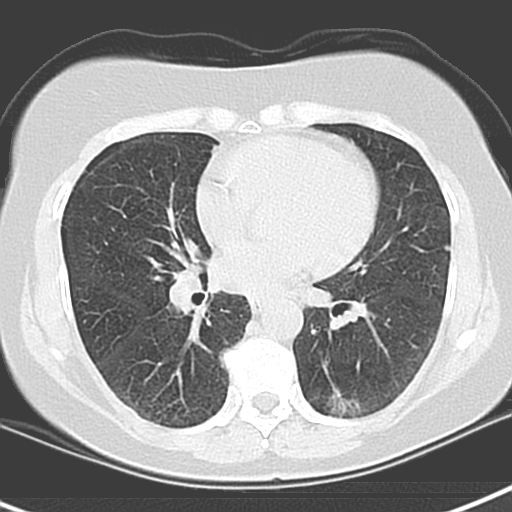
Axial slice from a low-dose chest CT screening exam, first (baseline) screen, lung window (W 1500 / L -600 HU), 3.2 mm slice thickness, slice 76 of 129 in the series, 512 × 512 image matrix. Female participant, aged 55 years at enrolment. Current smoker at enrolment.
- Expert-annotated lung lesion, bounding box (x1, y1, x2, y2) in pixels: (314, 374, 390, 423).
- The screening reader recorded 3 non-calcified nodules or masses ≥4 mm on this exam; which of them this box marks is not recorded.
- Official screen result: positive, change unspecified: nodule(s) >= 4 mm or enlarging nodule(s), mass(es), or other non-specific abnormalities suspicious for lung cancer.
- Lung cancer was diagnosed 1063 days after this screen (after the third annual screen): adenocarcinoma with mixed subtypes, left lower lobe, poorly differentiated (G3), stage IA (AJCC 6th edition), 21 mm at pathology.